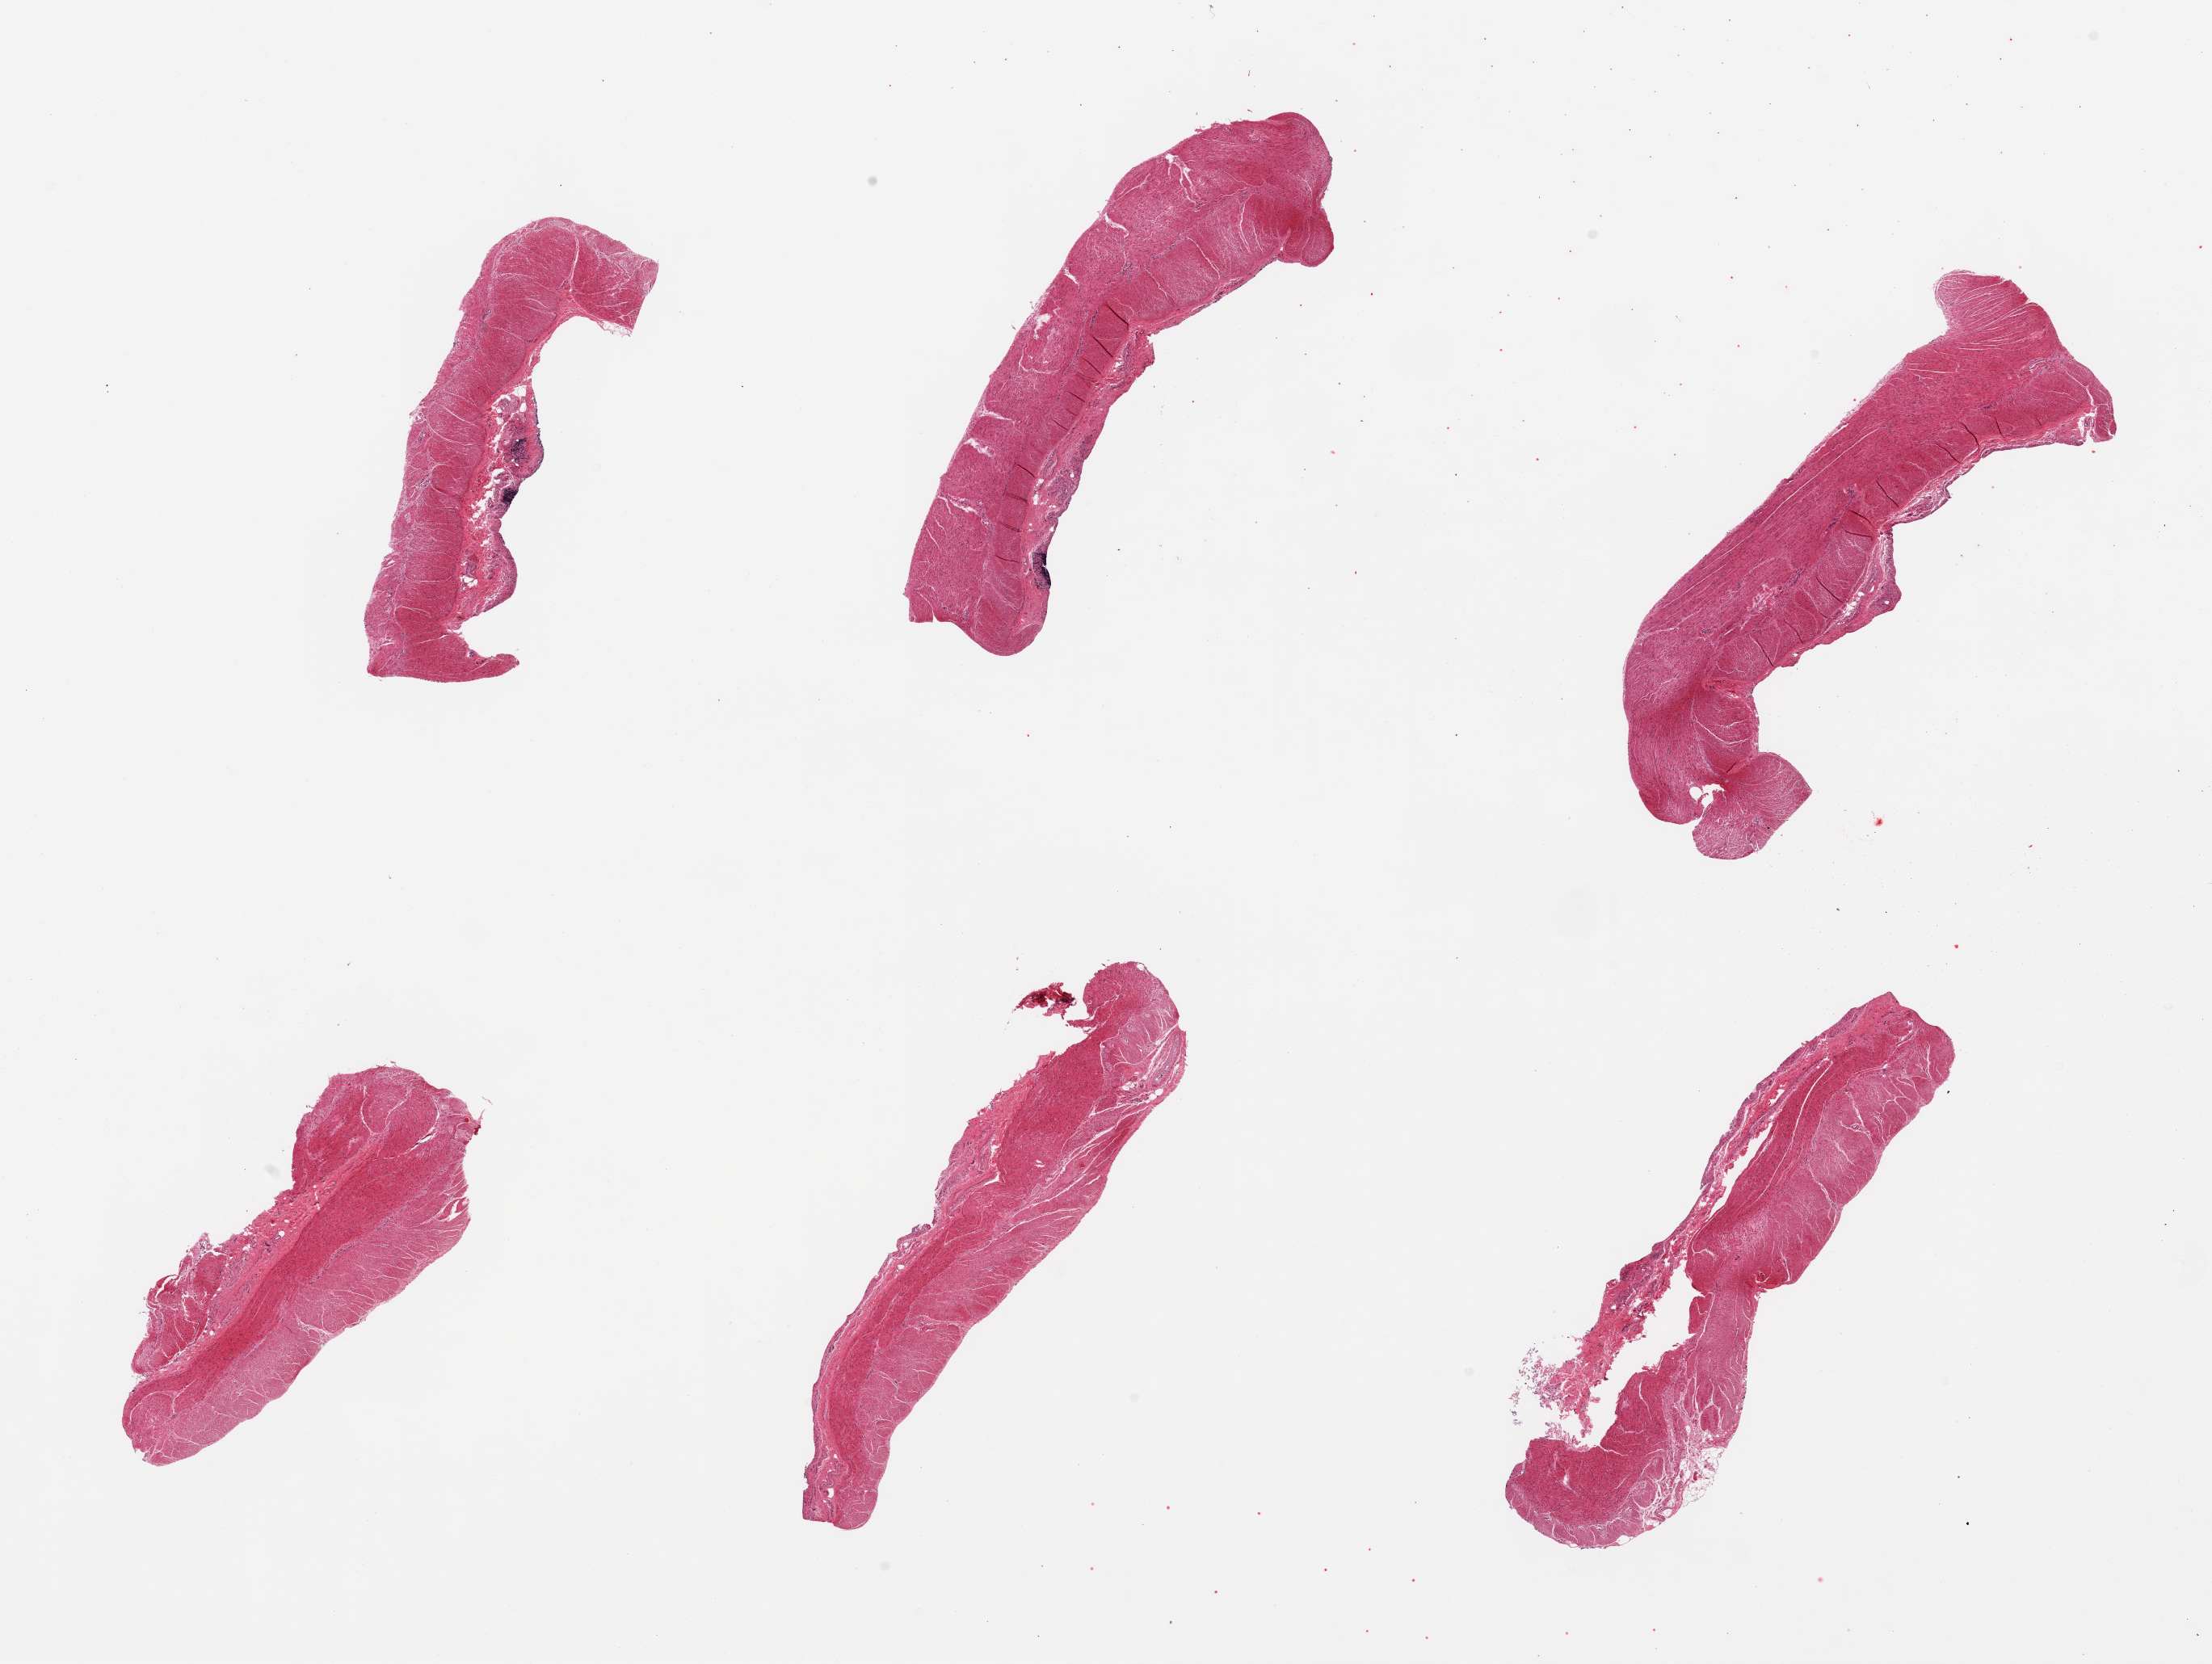
Hematoxylin and eosin (H&E) whole-slide image — low-resolution overview of the scanned area, about 21.7 x 16.3 mm, PAXgene-fixed, paraffin-embedded tissue, sampled site (target tissue): sigmoid colon, donor tissue sample. Donor: female.
- review note (as recorded): 6 pieces; muscle with focal submucosal elements